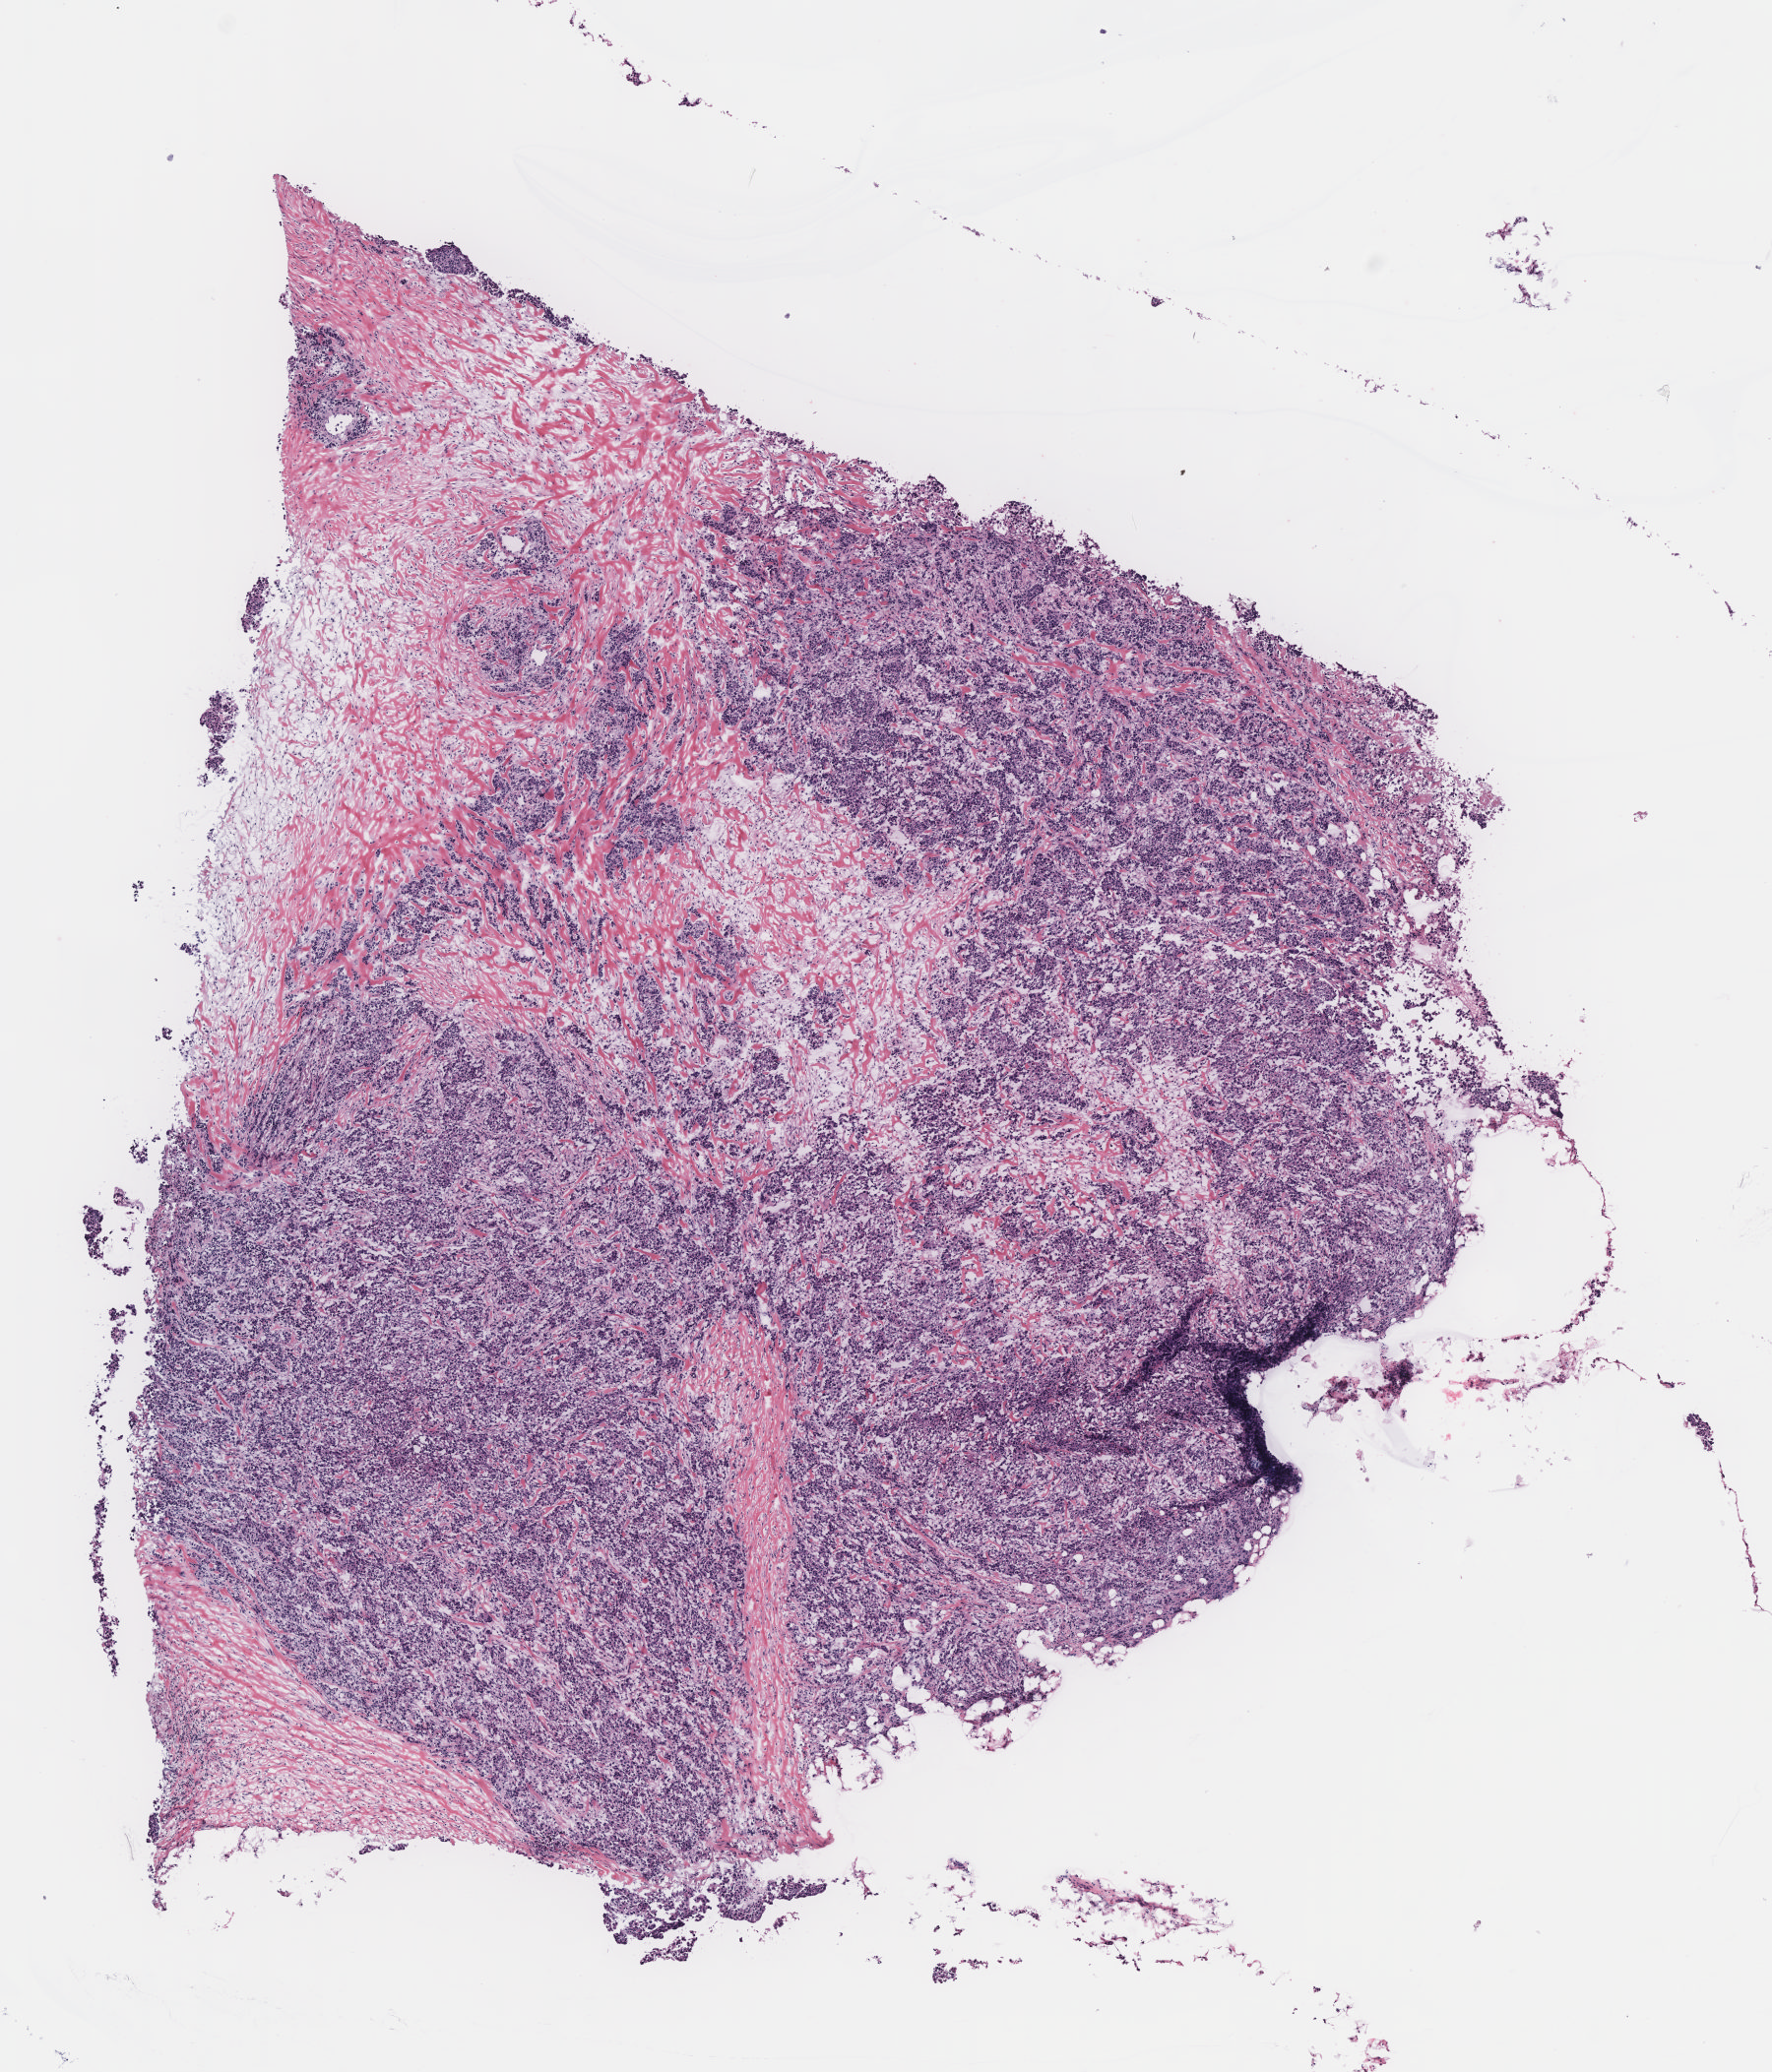
H&E whole-slide image, shown as a low-resolution overview of the whole scanned area (about 7.2 x 8.4 mm), breast, tumour tissue. Female, 75 y/o.
- AJCC pathologic stage: IIIB
- histologic diagnosis: Infiltrating duct carcinoma, NOS